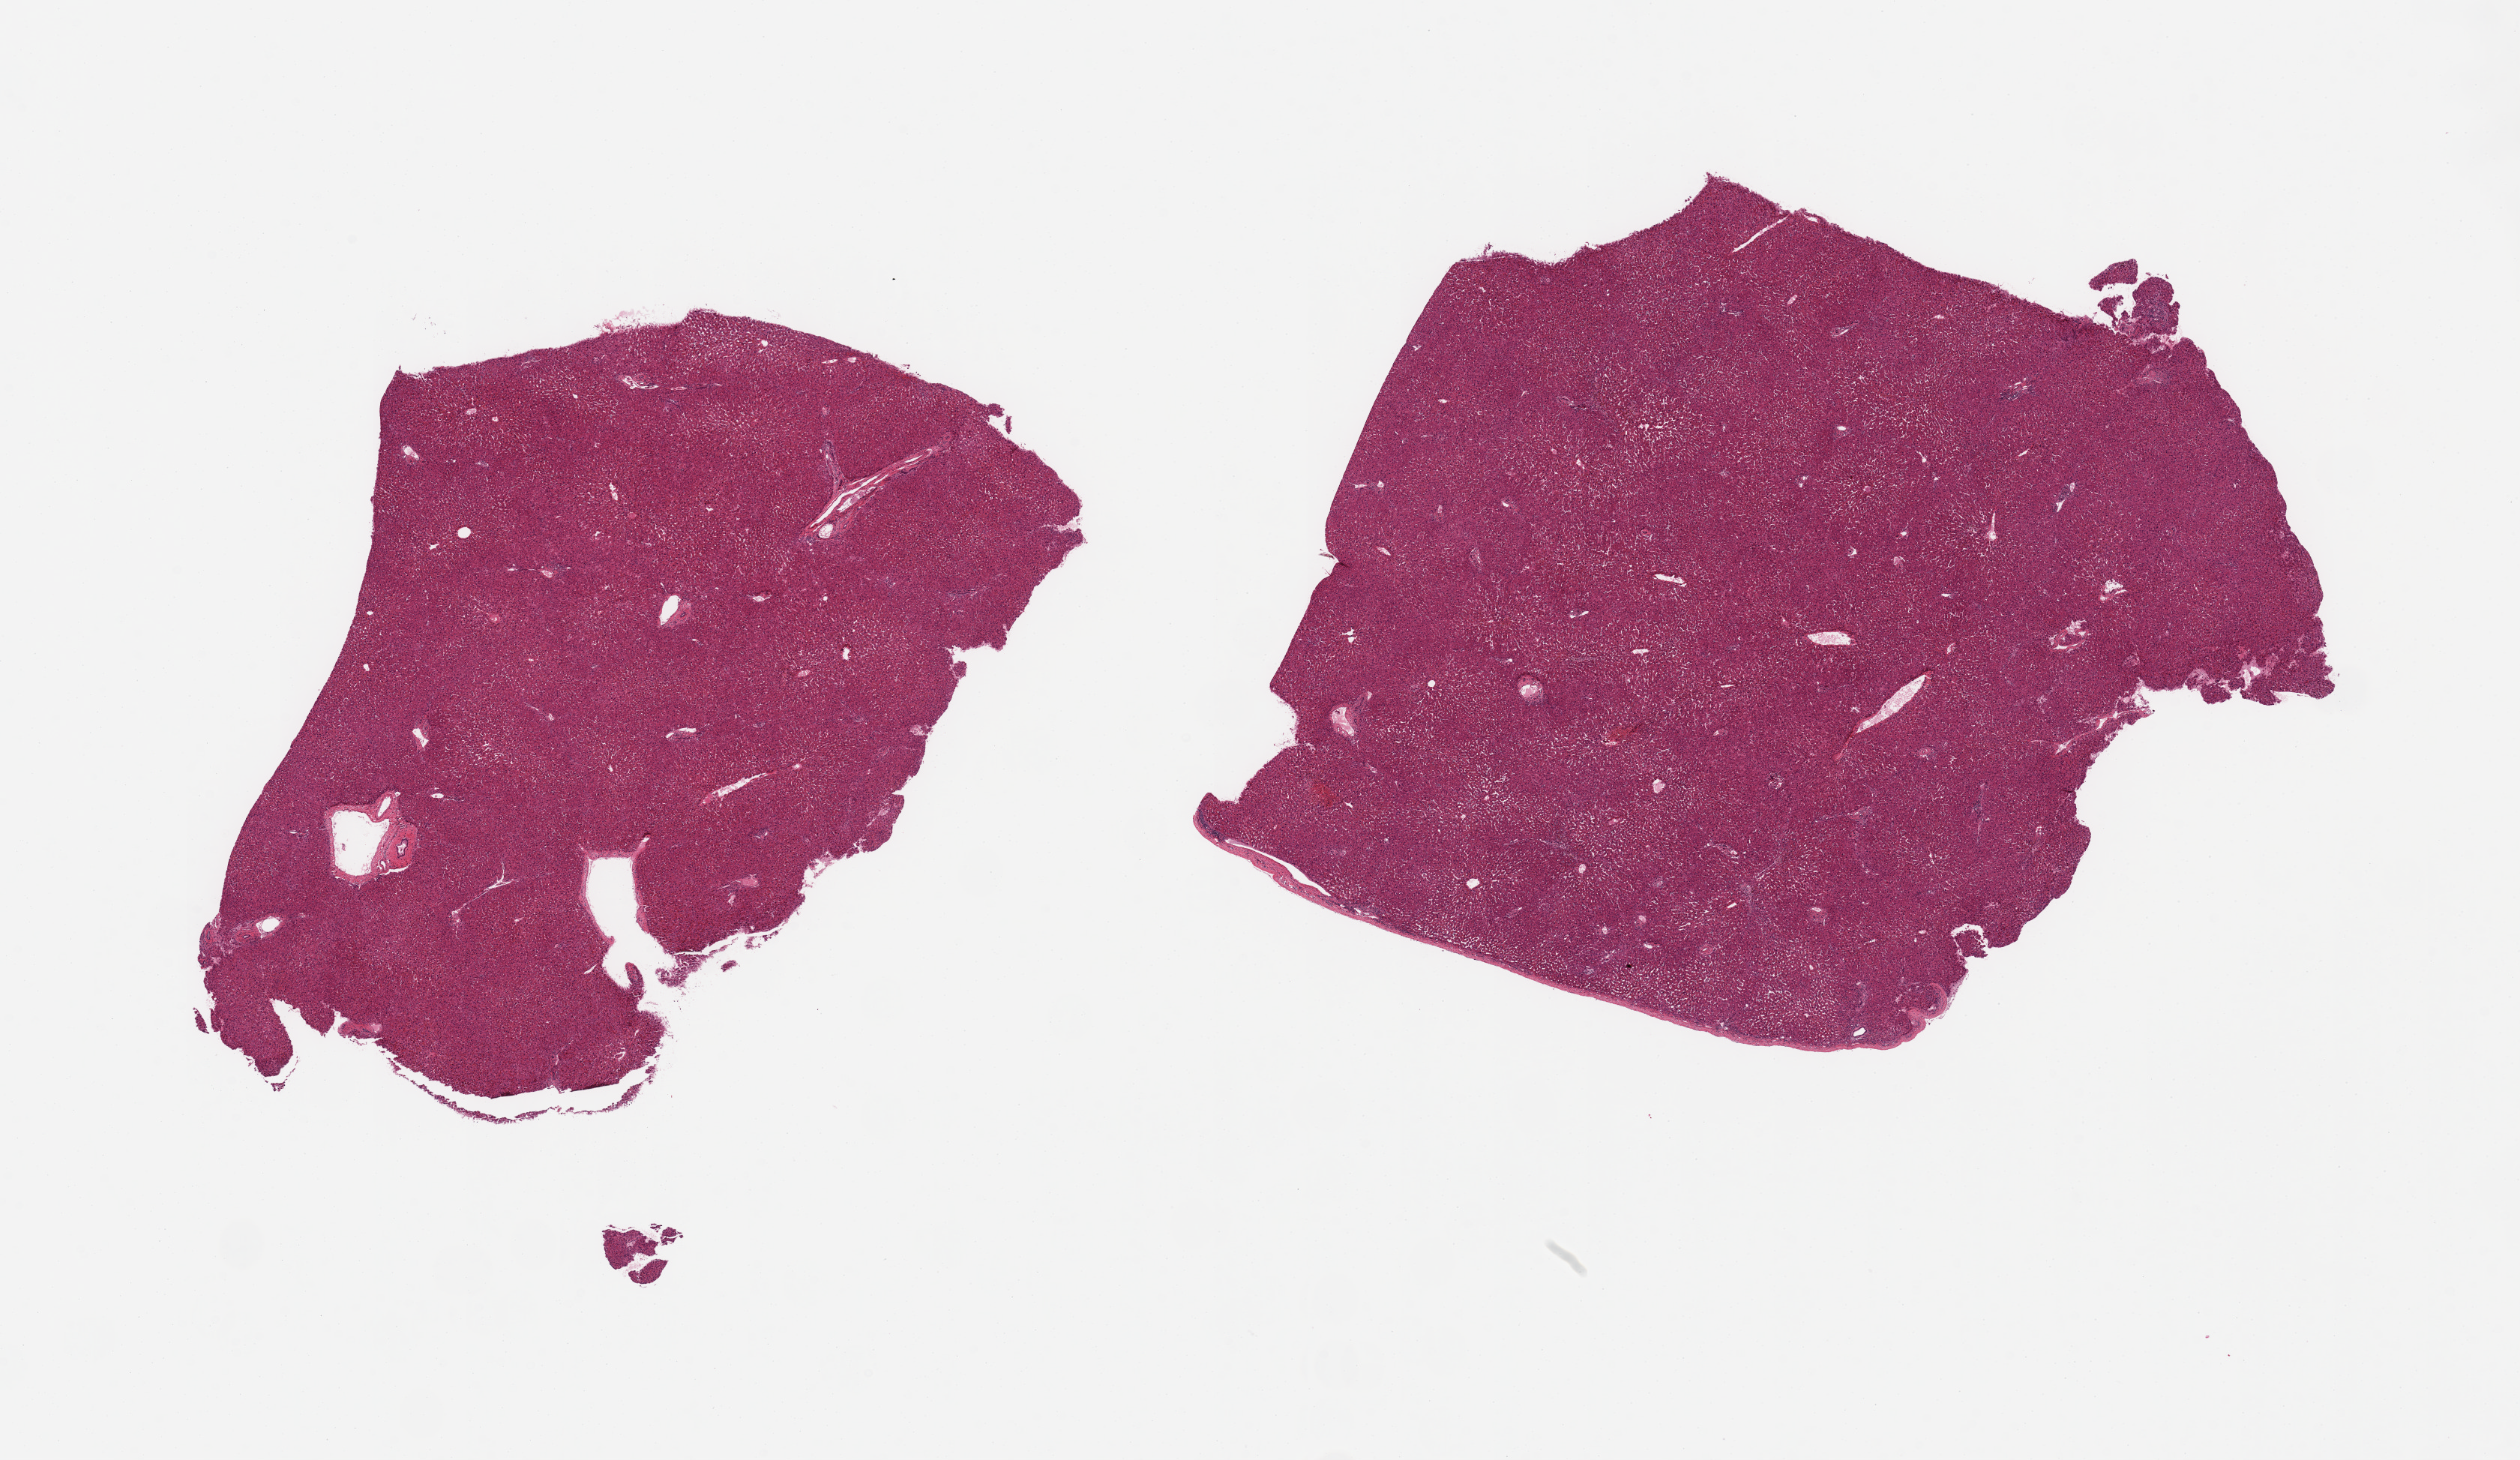
Hematoxylin and eosin (H&E) whole-slide image, low-resolution overview of the scanned area, about 26.6 x 15.4 mm. PAXgene-fixed paraffin-embedded (PFPE) section. Section of liver (target tissue). Donor tissue sample. Donor: male.
Review note (as recorded): 2 pieces, polymorphonuclear cells in sinuosoids and mild portal and lobular chronic inflammation. Reviewed by NIH consult panel.